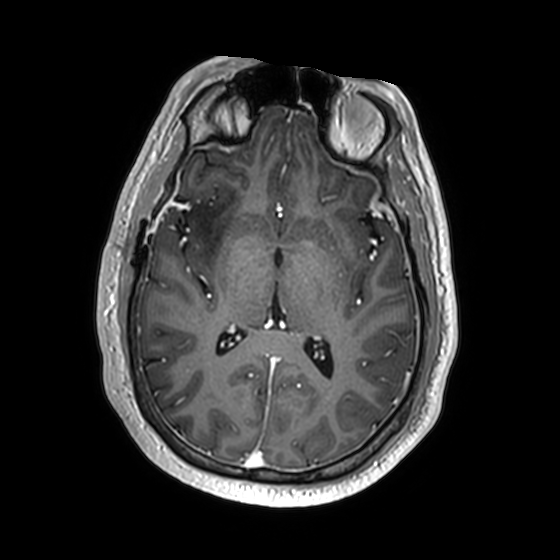
Brain MRI from a brain-tumour surgery series, one axial slice. T1-weighted post-contrast. 1 mm slice thickness. 560 × 560 image matrix, field of view 256 × 256 mm. From the clinical record (not read from this slice): histopathology: Astrocytoma; WHO grade: 2; IDH mutation: yes; tumour location: Right Insular.
Outlined on this slice (manually delineated by an expert):
- previous resection cavity: bounding box [x1, y1, x2, y2] px = [178, 198, 188, 203]